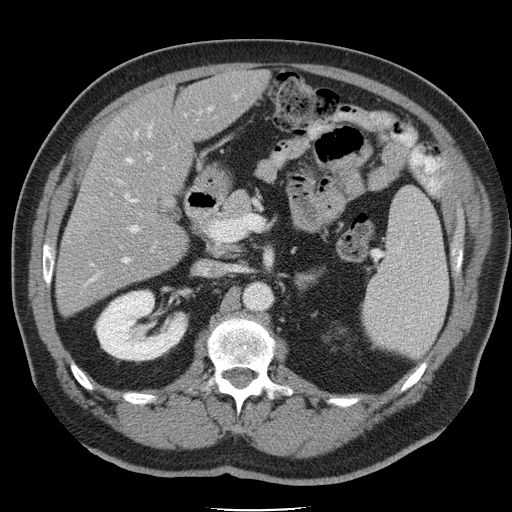
Contrast-enhanced abdominal CT, one axial slice. Slice 22 of 45 in the series (ordered by position). 120 kVp. Intravenous contrast given. Soft-tissue window (W 400 / L 40 HU). 512 × 512 image matrix, field of view 386 × 386 mm. Male patient, age 65 years. Case-level facts recorded for this patient, not image findings: diagnosis: colorectal cancer liver metastases, imaged before liver resection; multiple liver metastases: yes; largest metastasis: 4.9 cm; disease in both lobes: no.
Outlined on this slice (expert manual segmentation):
- hepatic veins: bounding box [x1, y1, x2, y2] px = [90, 95, 237, 281]
- liver: [56, 71, 267, 314]
- planned liver remnant (the part of the liver to remain after resection): [98, 71, 267, 191]
- portal vein (with intrahepatic branches): [125, 132, 152, 232]